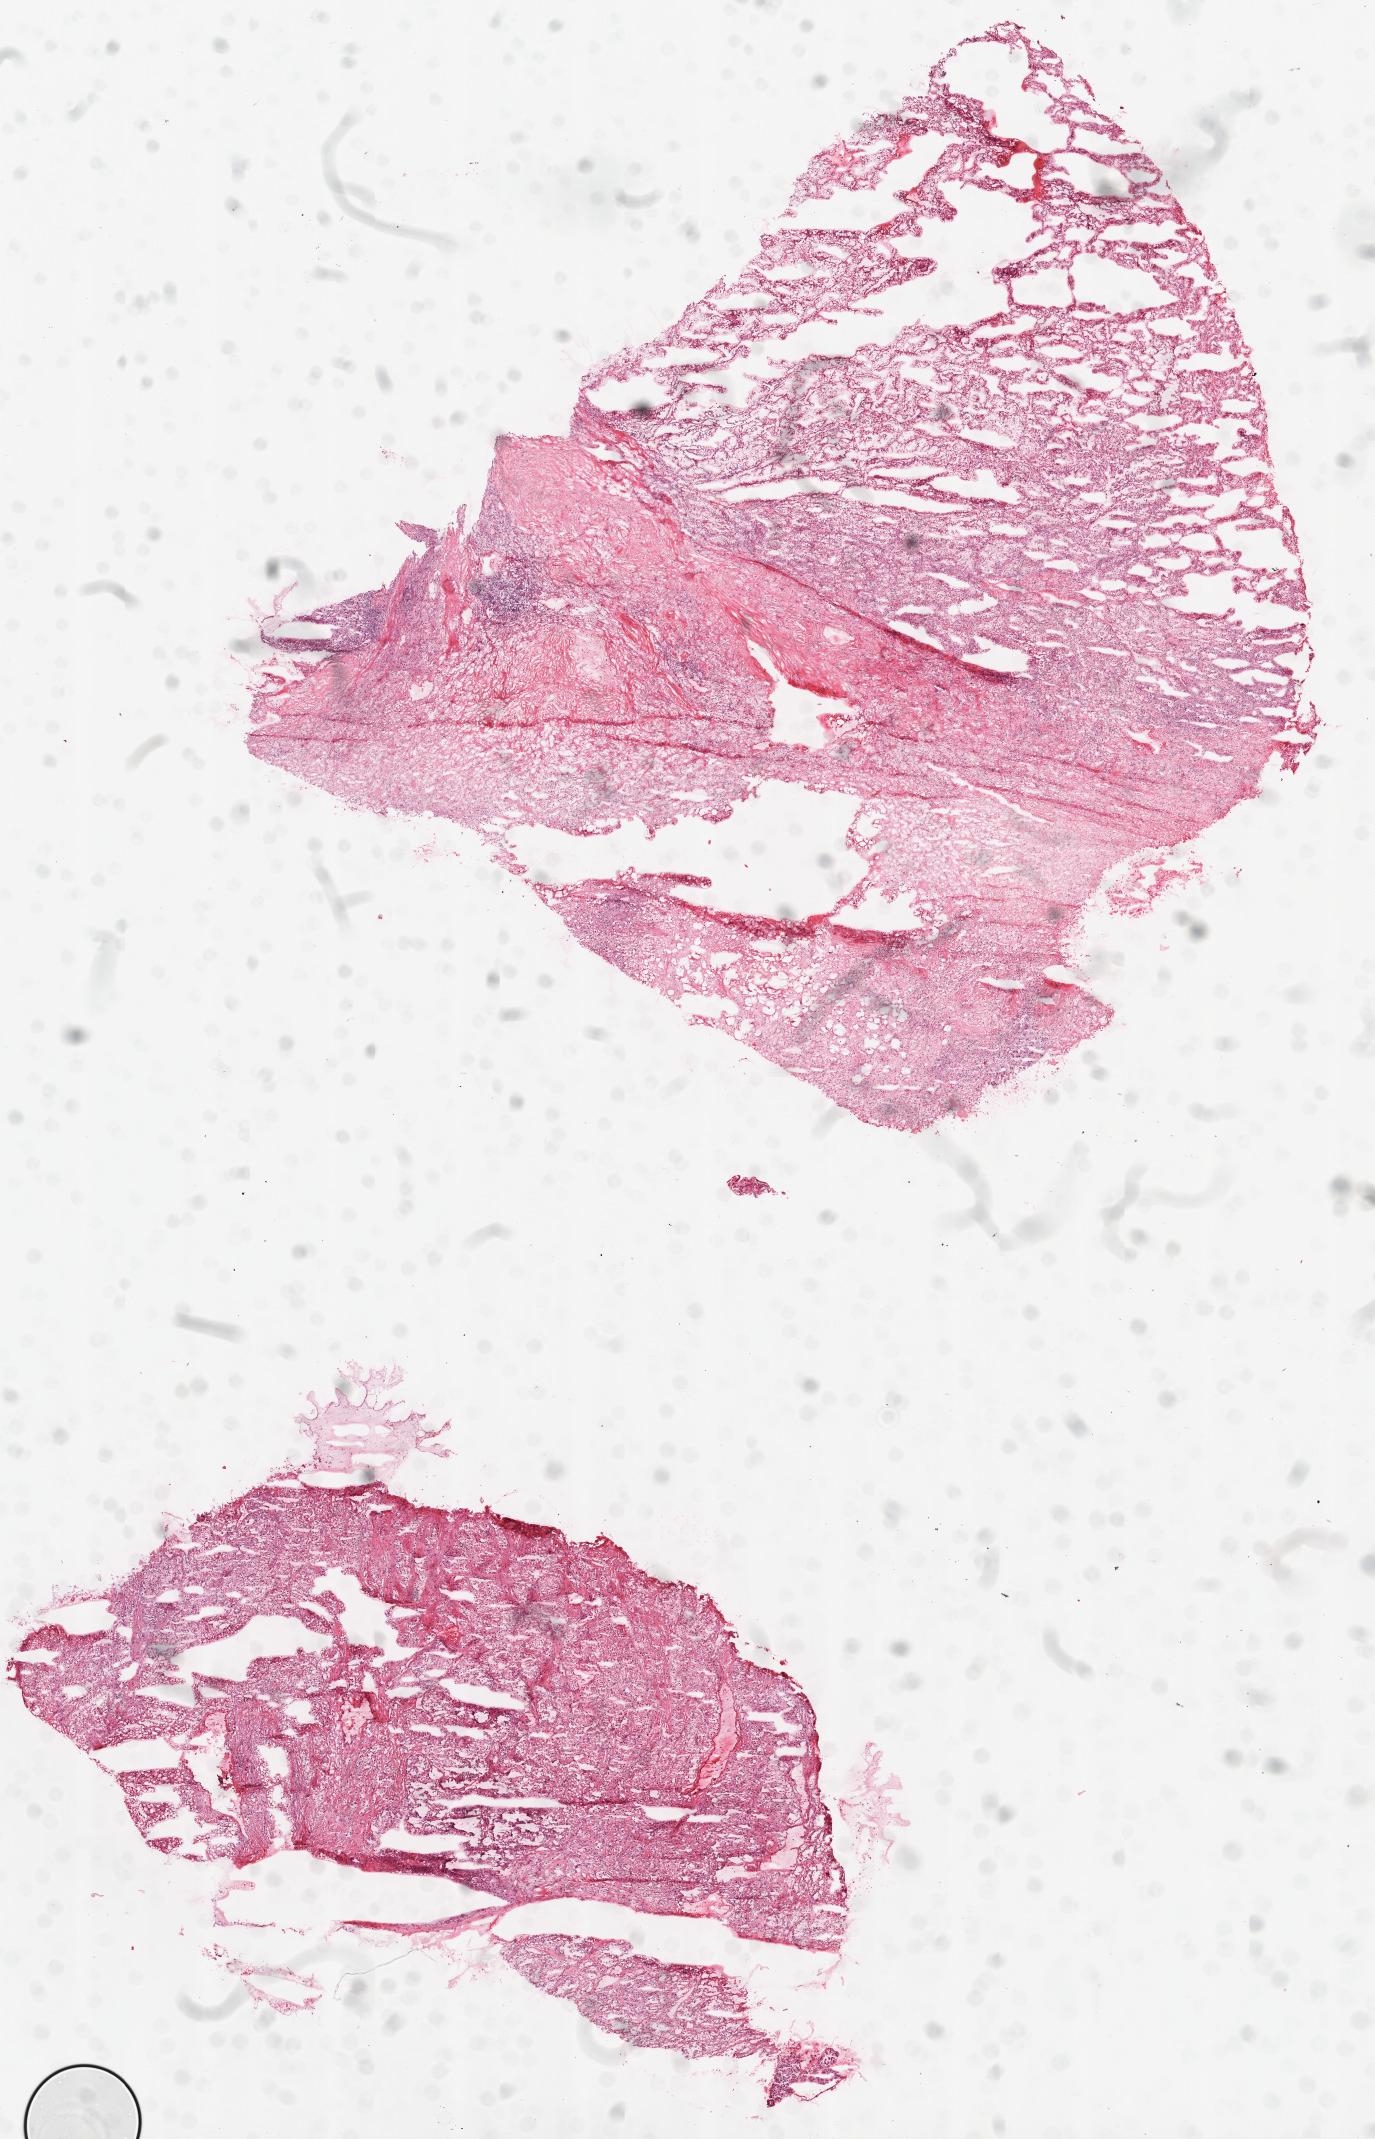
Whole-slide histology image, H&E — whole scanned area (about 11.0 x 17.2 mm, acquisition: 20x scan) shown as a low-resolution overview. Frozen section from the top of the tissue portion. Primary tumour sample from the kidney. Patient: male, age at initial diagnosis 72 years. Histologic grade: G4 (undifferentiated). Pathologist review of this section (percent, as recorded): tumour cells 80%, tumour nuclei 80%, normal cells 0%, stromal cells 20%, necrosis 0%.
- AJCC pathologic stage: III
- laterality: left
- pathologic diagnosis: Clear cell adenocarcinoma, NOS